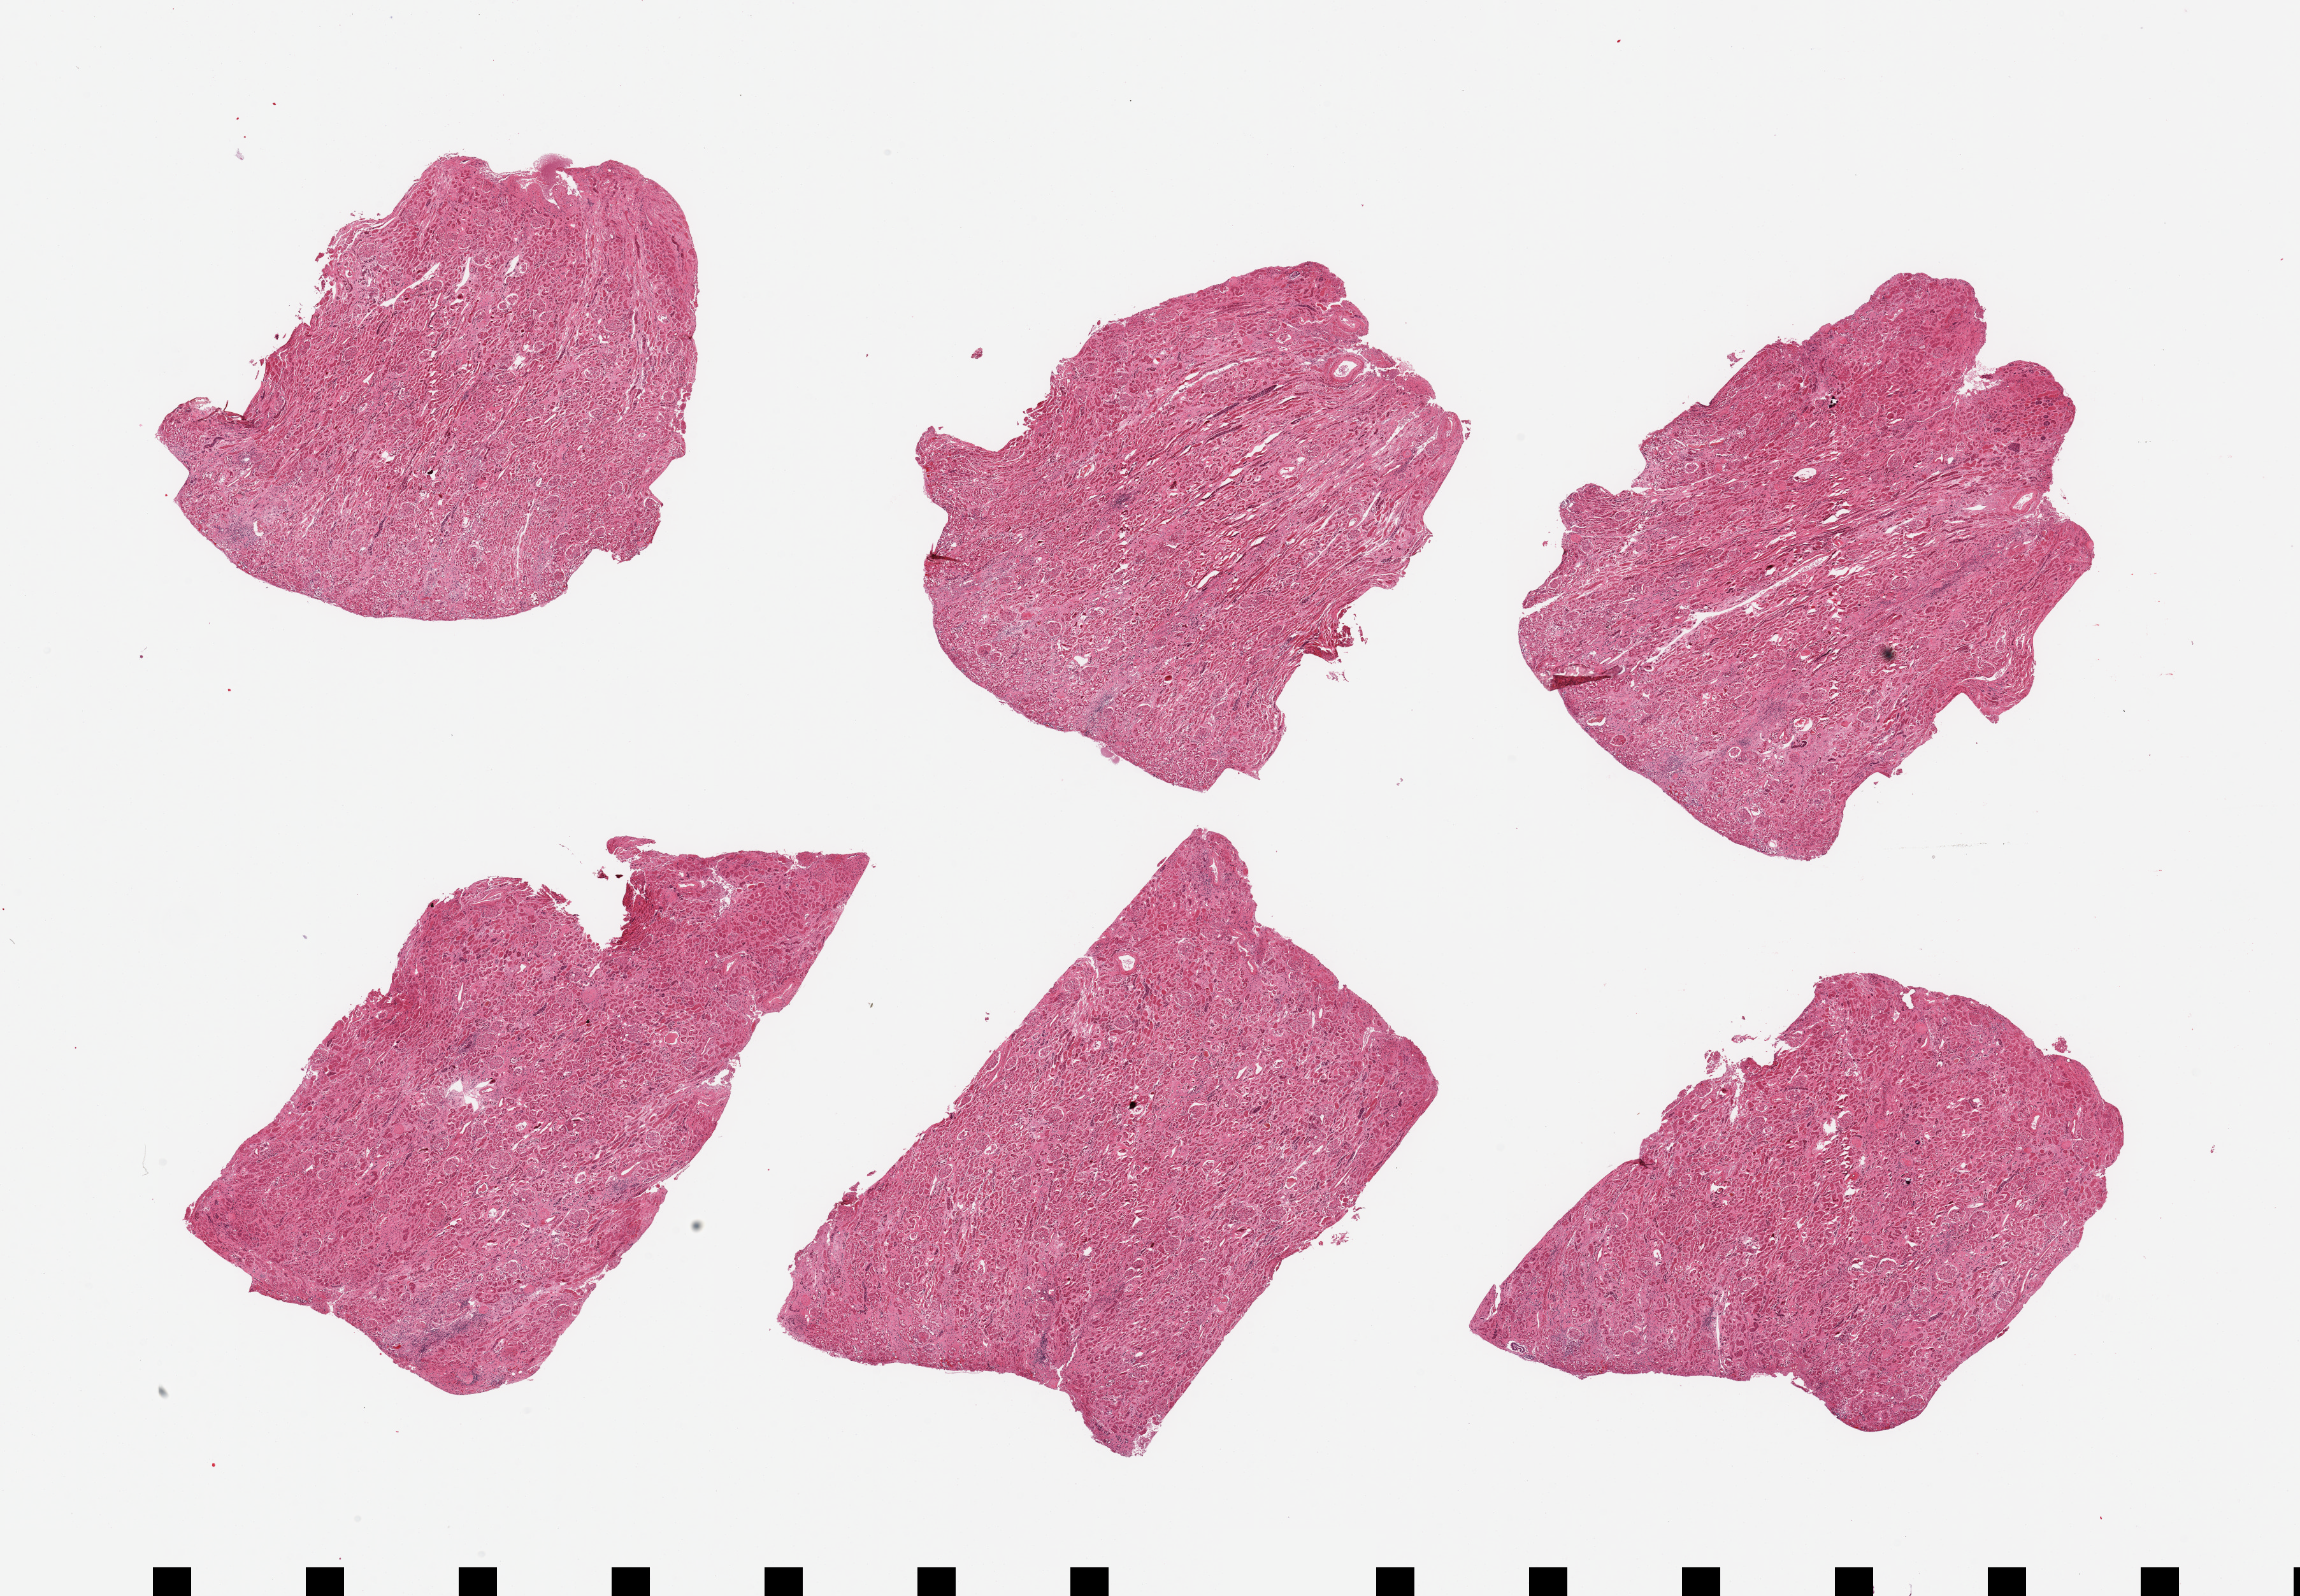
H&E whole-slide image, a low-resolution overview of the entire scanned area, about 28.5 x 19.8 mm (slide scanned at 20x); PAXgene-fixed, paraffin-embedded tissue; sampled site (target tissue): renal cortex; tissue donor sample. Male donor.
- pathologist's review note for this sample: 6 pieces, glomeruli present, tubular necrosis/autolysis is advanced